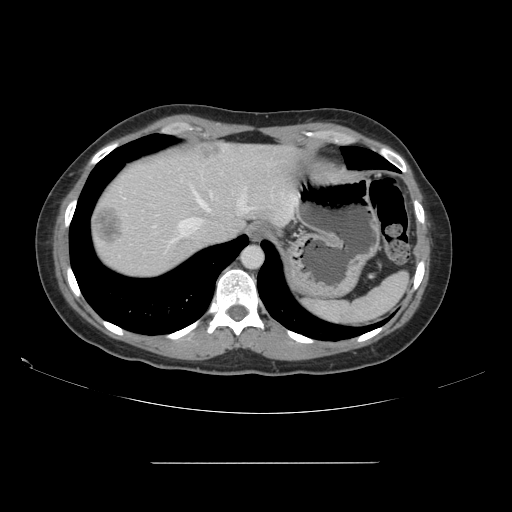
Contrast-enhanced abdominal CT, one axial slice. Intravenous contrast given. Soft-tissue window (W 400 / L 40 HU). 2.5 mm slice thickness. 512 × 512 image matrix. Female patient, age 46 years. From the clinical record (not read from this slice): diagnosis: colorectal cancer liver metastases, imaged before liver resection; multiple liver metastases: yes; largest metastasis: 3 cm; chemotherapy before resection: no.
Structures marked on this image (manually delineated by an expert):
- hepatic veins: bounding box <171,189,252,243> (left, top, right, bottom; pixels)
- liver: <91,144,292,278>
- planned liver remnant (the part of the liver to remain after resection): <103,146,293,240>
- liver metastasis: <95,205,123,244>
- liver metastasis: <198,146,224,159>